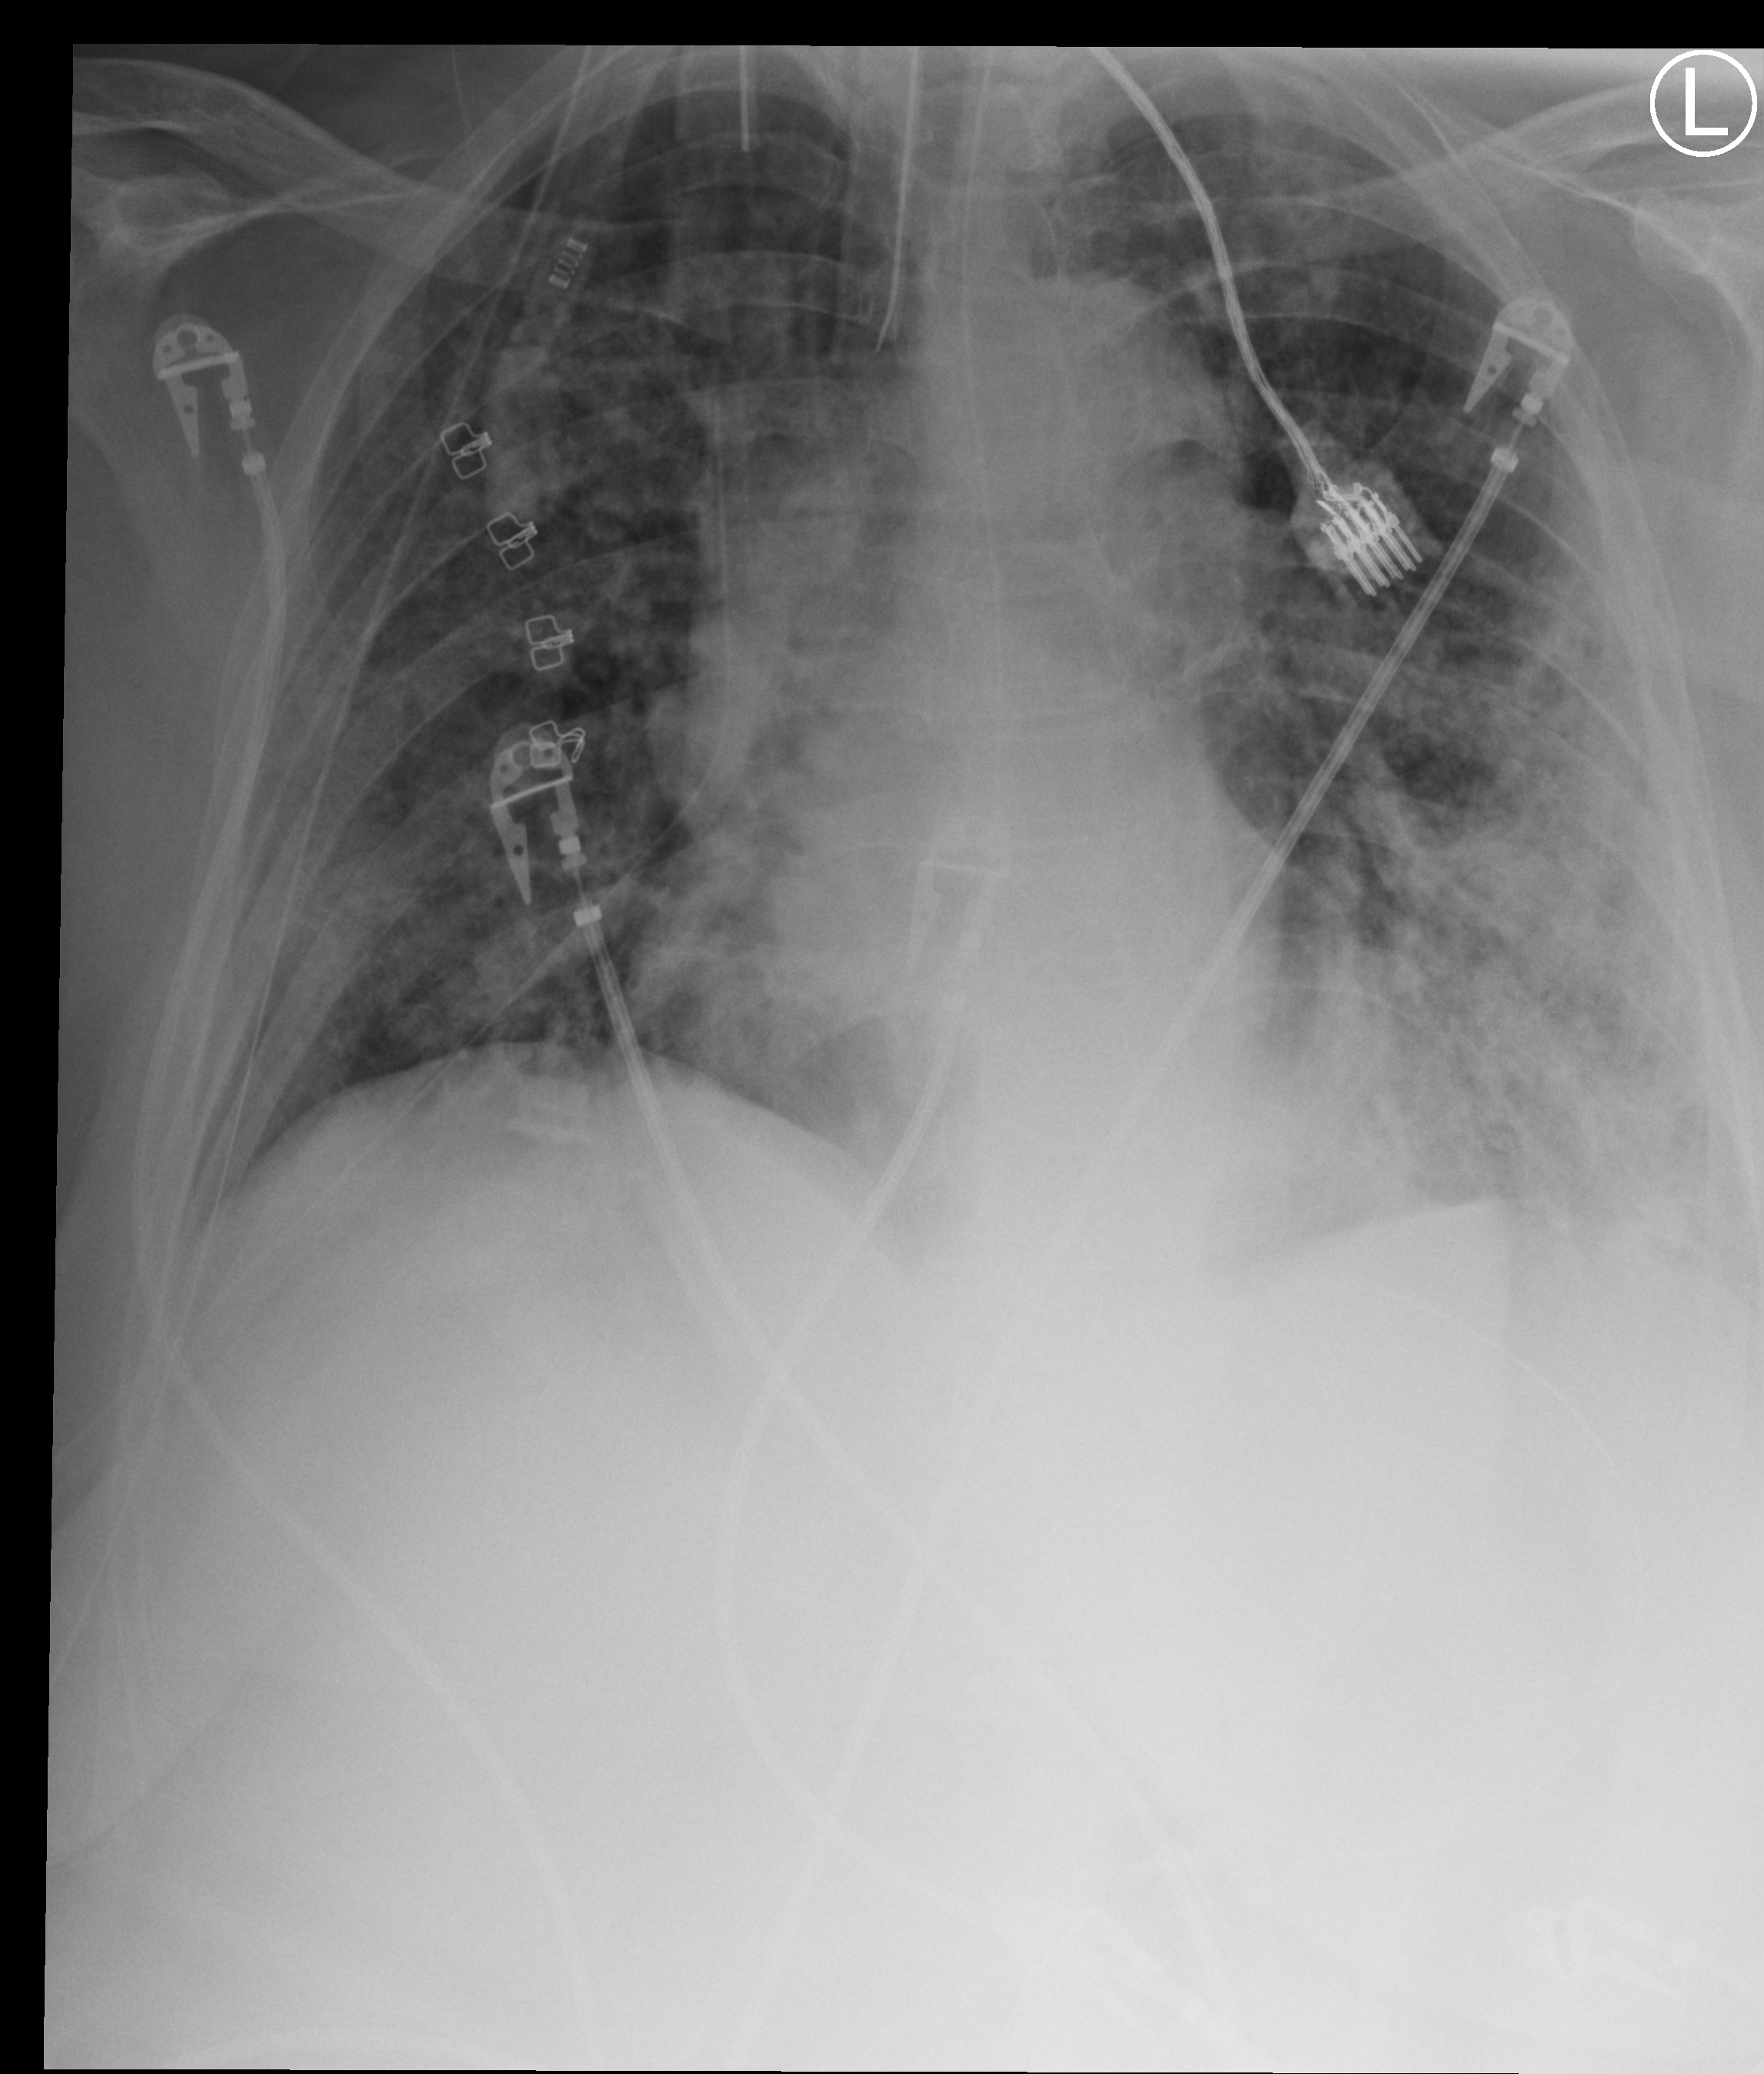
Portable chest radiograph; anteroposterior (AP) projection. Female patient hospitalised with COVID-19, age 60–74 years.
From the hospital-stay record, not from the radiograph (when in the stay this image was taken is not recorded): mechanically ventilated during this hospital stay: yes.